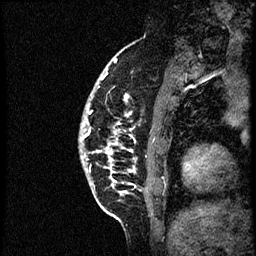
Breast MRI (dynamic contrast-enhanced), one sagittal slice; slice 12 of 56 in the series (ordered by position); dynamic contrast-enhanced study with each time point stored as its own series, time point 2 of 3 at this slice position (early post-contrast, ordered by acquisition time); 1.5 T; TE 4.2 ms, TR 21.3 ms; 2 mm slice thickness; 256 × 256 image matrix, field of view 200 × 200 mm. Female patient, age 41 years. Case-level facts recorded for this patient, not image findings: setting: breast cancer imaged before/during neoadjuvant chemotherapy; receptor status: HER2-positive.
Annotated regions visible in this slice (semi-automatically segmented with operator editing):
- analysis volume of interest (the breast-tissue region the enhancement analysis was run in; not a lesion): bounding box (x1, y1, x2, y2) in pixels: (78, 73, 177, 205)
- tumour enhancement mask (voxels above the 100 % enhancement threshold inside the analysis volume of interest): (82, 75, 119, 169)